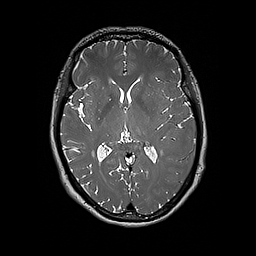
Brain MRI from a brain-tumour surgery series, one axial slice; position 102 of 192 along the scan axis; 1 mm slice thickness; 256 × 256 image matrix, field of view 250 × 250 mm. Case-level facts recorded for this patient, not image findings: histopathology: Glioblastoma; WHO grade: 4; IDH mutation: no.
Annotated regions visible in this slice (expert manual segmentation):
- tumour: bounding box (x1, y1, x2, y2) in pixels: (183, 161, 186, 164)